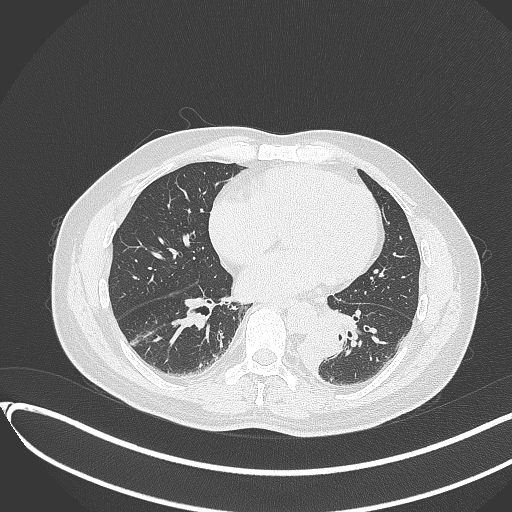
Chest CT, one axial slice; position 133 of 417 along the scan axis; 120 kVp; lung window (W 1500 / L -600 HU); 1 mm slice thickness; 512 × 512 image matrix, field of view 400 × 400 mm. Male patient, age 54 years. From the clinical record (not read from this slice): clinical TNM (as recorded): T3 N0 M0.
Annotated regions visible in this slice (bounding box drawn by a radiologist):
- lung tumour (recorded histology: squamous cell carcinoma): bounding box (x1, y1, x2, y2) in pixels: (299, 313, 349, 371)